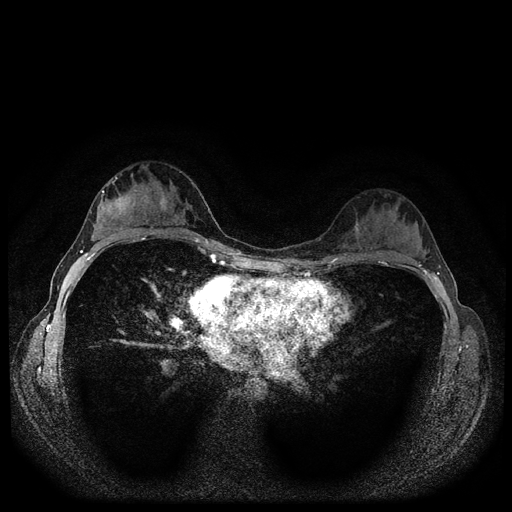
Breast MRI (dynamic contrast-enhanced, multi-phase), one axial slice; position 66 of 116 along the scan axis; dynamic contrast-enhanced series, time point 2 of 5 at this slice position (early post-contrast); 1.5 T; TE 2.7 ms, TR 5.4 ms; 512 × 512 image matrix, field of view 320 × 320 mm. Female patient, age 29 years.
Annotated regions visible in this slice (semi-automatically segmented with operator editing):
- breast lesion (labelled benign in the annotation): bounding box <159,196,169,212> (left, top, right, bottom; pixels)
- breast lesion (labelled 'tumour' in the annotation; benign lesions carry a separate 'benign' label): <105,189,136,218>